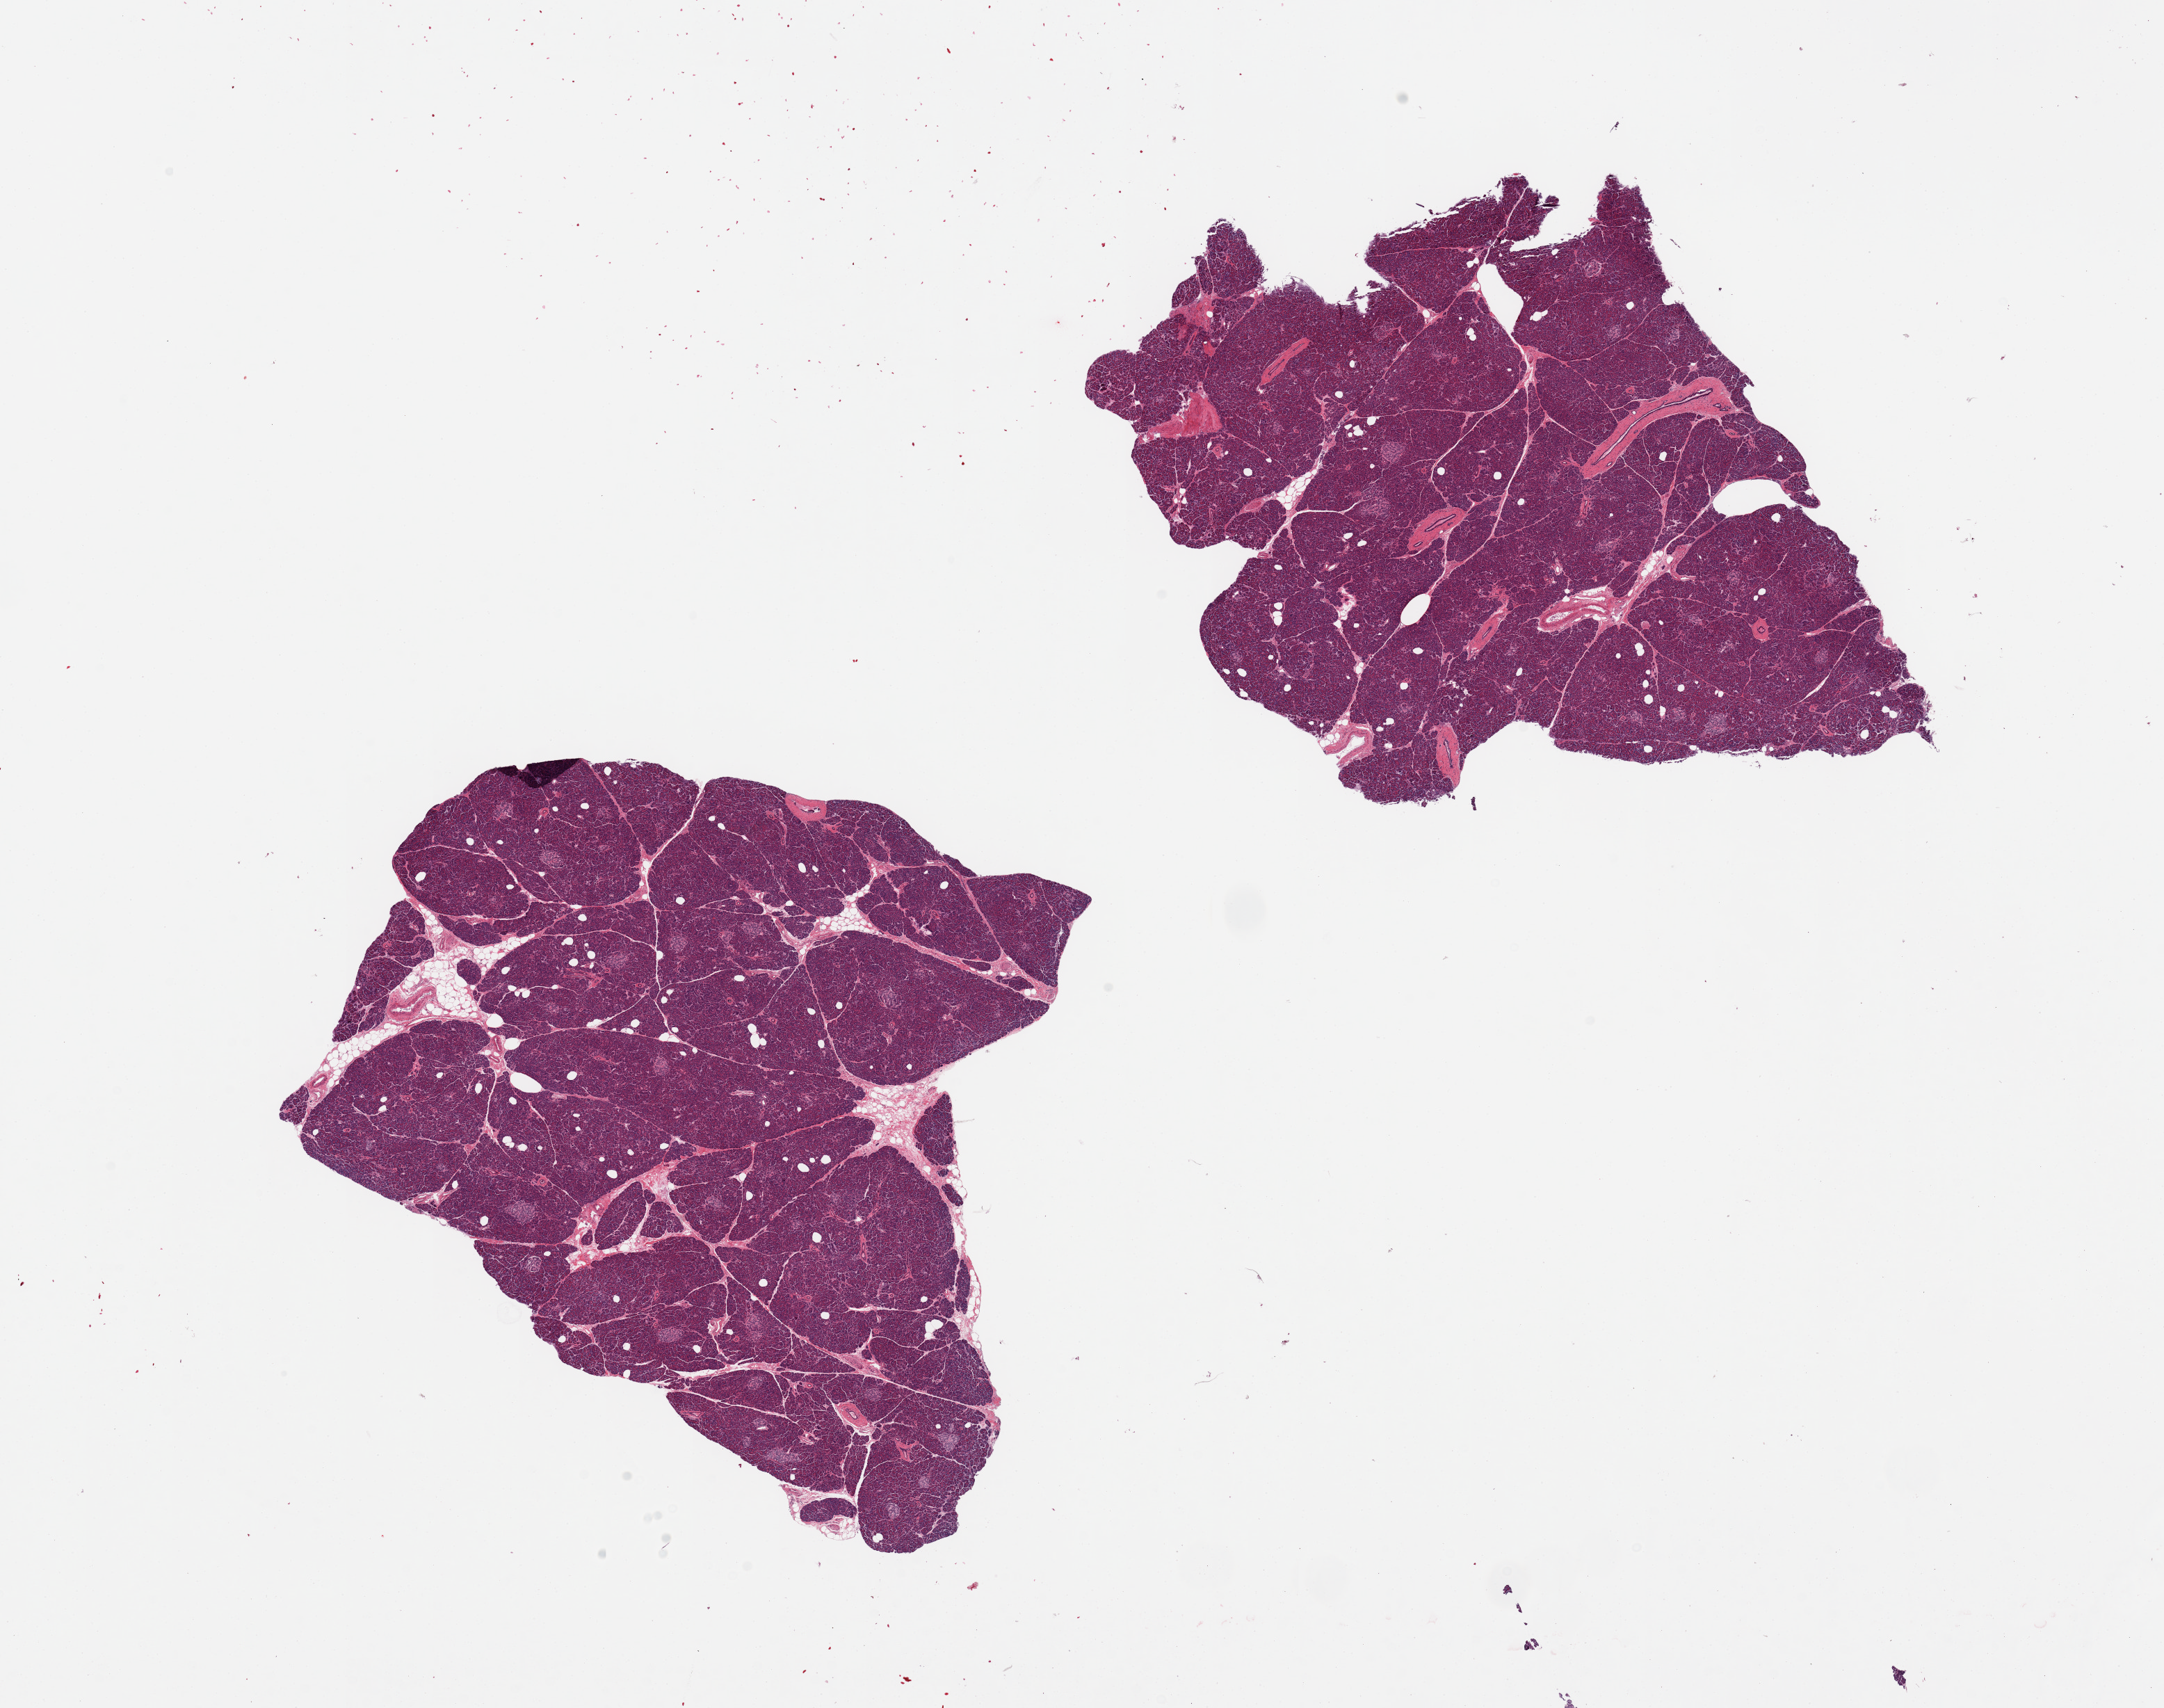
Hematoxylin and eosin (H&E) whole-slide image, whole scanned area (about 24.6 x 19.4 mm, from a 20x scan) shown as a low-resolution overview, PAXgene-fixed, paraffin-embedded tissue, section of pancreas (target tissue), donor tissue sample. Donor: female.
• review note (as recorded): 2 pieces, extremely well- preserved; Islets well visualized; minimal fat, good specimens